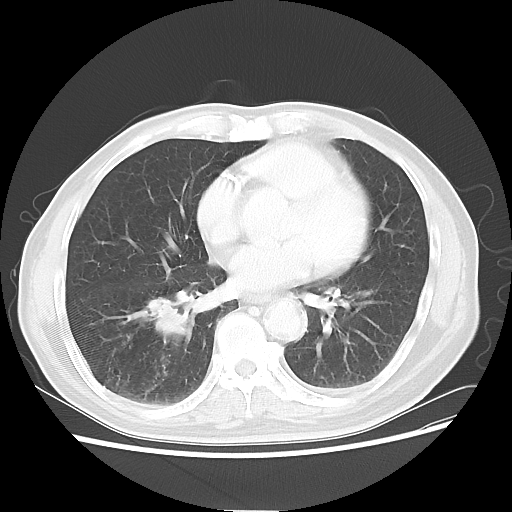
Chest CT, one axial slice; position 25 of 58 along the scan axis; lung window (W 1500 / L -600 HU); 5 mm slice thickness; 512 × 512 image matrix, field of view 360 × 360 mm. Patient: male, 74 years. Case-level facts recorded for this patient, not image findings: clinical TNM (as recorded): T1c N1 M1.
Annotated regions visible in this slice (bounding box drawn by a radiologist):
- lung tumour (recorded histology: adenocarcinoma): bounding box <126,291,194,349> (left, top, right, bottom; pixels)